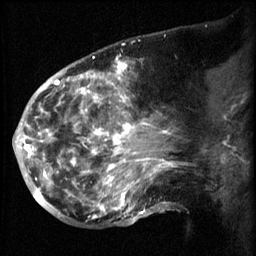
Breast MRI (dynamic contrast-enhanced), one sagittal slice. Slice 28 of 60 in the series (ordered by position). 3 images stored at this slice position (order not interpretable as contrast timing). 1.5 T. TE 4.2 ms, TR 8.2 ms. 2.3 mm slice thickness. 256 × 256 image matrix, field of view 200 × 200 mm. Patient: female, 50 years.
Outlined on this slice (semi-automatic segmentation, software-assisted and operator-edited):
- analysis volume of interest (the breast-tissue region the enhancement analysis was run in; not a lesion): box from (x=50, y=64) to (x=169, y=217) px
- tumour enhancement mask (voxels above the 70 % enhancement threshold inside the analysis volume of interest): (x=50, y=64)–(x=169, y=217)